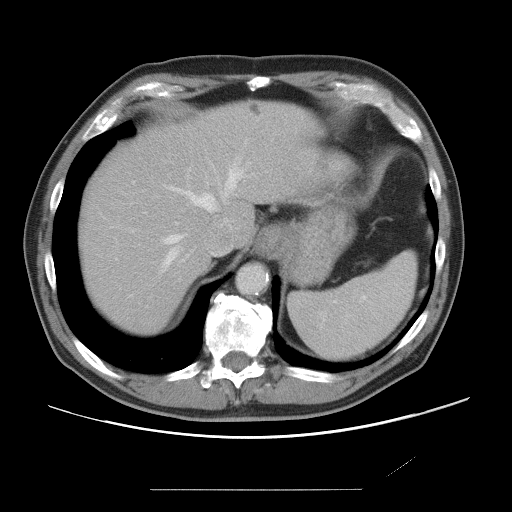
Contrast-enhanced abdominal CT, one axial slice. Slice 60 of 87 in the series (ordered by position). Intravenous contrast given. Soft-tissue window (W 400 / L 40 HU). 5 mm slice thickness. 512 × 512 image matrix, field of view 406 × 406 mm. Male patient, age 74 years. From the clinical record (not read from this slice): diagnosis: colorectal cancer liver metastases, imaged before liver resection; multiple liver metastases: yes; largest metastasis: 1.1 cm; disease in both lobes: no.
Annotated regions visible in this slice (expert manual segmentation):
- hepatic veins: box from (x=132, y=167) to (x=243, y=266) px
- liver: (x=79, y=102)–(x=316, y=334)
- planned liver remnant (the part of the liver to remain after resection): (x=79, y=102)–(x=317, y=335)
- portal vein (with intrahepatic branches): (x=116, y=222)–(x=178, y=260)
- liver metastasis: (x=249, y=103)–(x=261, y=115)